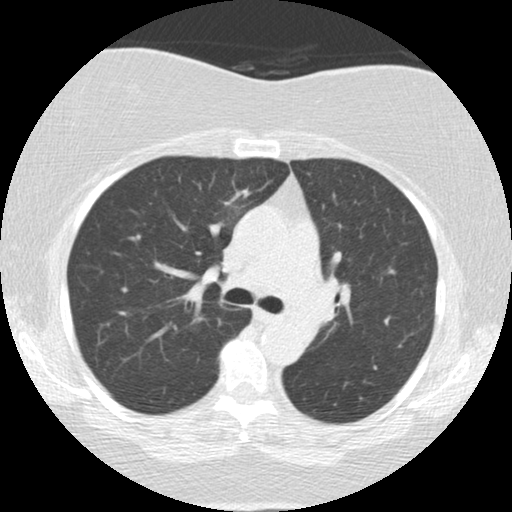
Low-dose screening chest CT, one axial slice. Position 86 of 136 along the scan axis. Reconstruction kernel STANDARD. 120 kVp. Lung window (W 1500 / L -600 HU). 2.5 mm slice thickness. 512 × 512 image matrix, field of view 309 × 309 mm.
Outlined on this slice (manually delineated by an expert):
- lesion 2 (tumor, mediastinum): bounding box (x1, y1, x2, y2) in pixels: (300, 280, 337, 327)